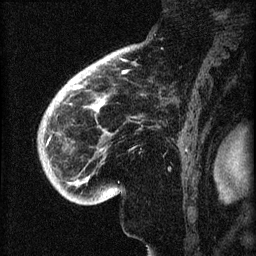
Breast MRI (dynamic contrast-enhanced), one sagittal slice. Slice 51 of 60 in the series (ordered by position). Dynamic contrast-enhanced series, image 2 of 3 at this slice position (ordered by acquisition). 1.5 T. TE 4.2 ms, TR 8.2 ms. 256 × 256 image matrix, field of view 180 × 180 mm. Patient: female, 71 years.
Outlined on this slice (semi-automatically segmented with operator editing):
- analysis volume of interest (the breast-tissue region the enhancement analysis was run in; not a lesion): bounding box [x1, y1, x2, y2] px = [40, 72, 144, 196]
- tumour enhancement mask (voxels above the 70 % enhancement threshold inside the analysis volume of interest): [46, 80, 100, 146]